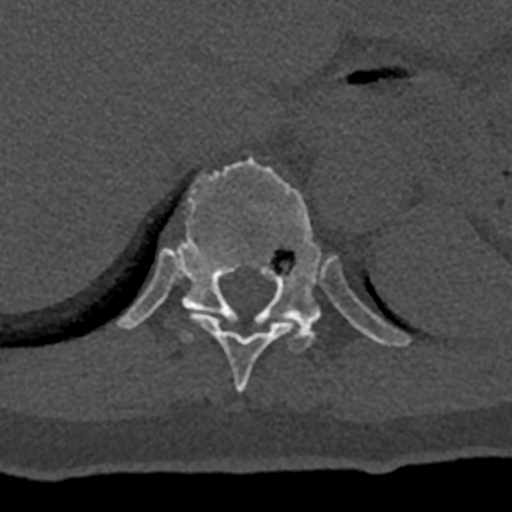
CT including the spine, one axial slice; position 572 of 797 along the scan axis; reconstruction kernel Br40s/3; bone window (W 1800 / L 400 HU); 0.5 mm slice thickness; 512 × 512 image matrix, field of view 160 × 160 mm. Male patient, age 74 years. Case-level facts recorded for this patient, not image findings: primary cancer: renal.
Annotated regions visible in this slice (semi-automatically segmented with operator editing):
- T10 vertebra: bounding box (x1, y1, x2, y2) in pixels: (190, 313, 292, 393)
- T11 vertebra: (117, 157, 410, 353)